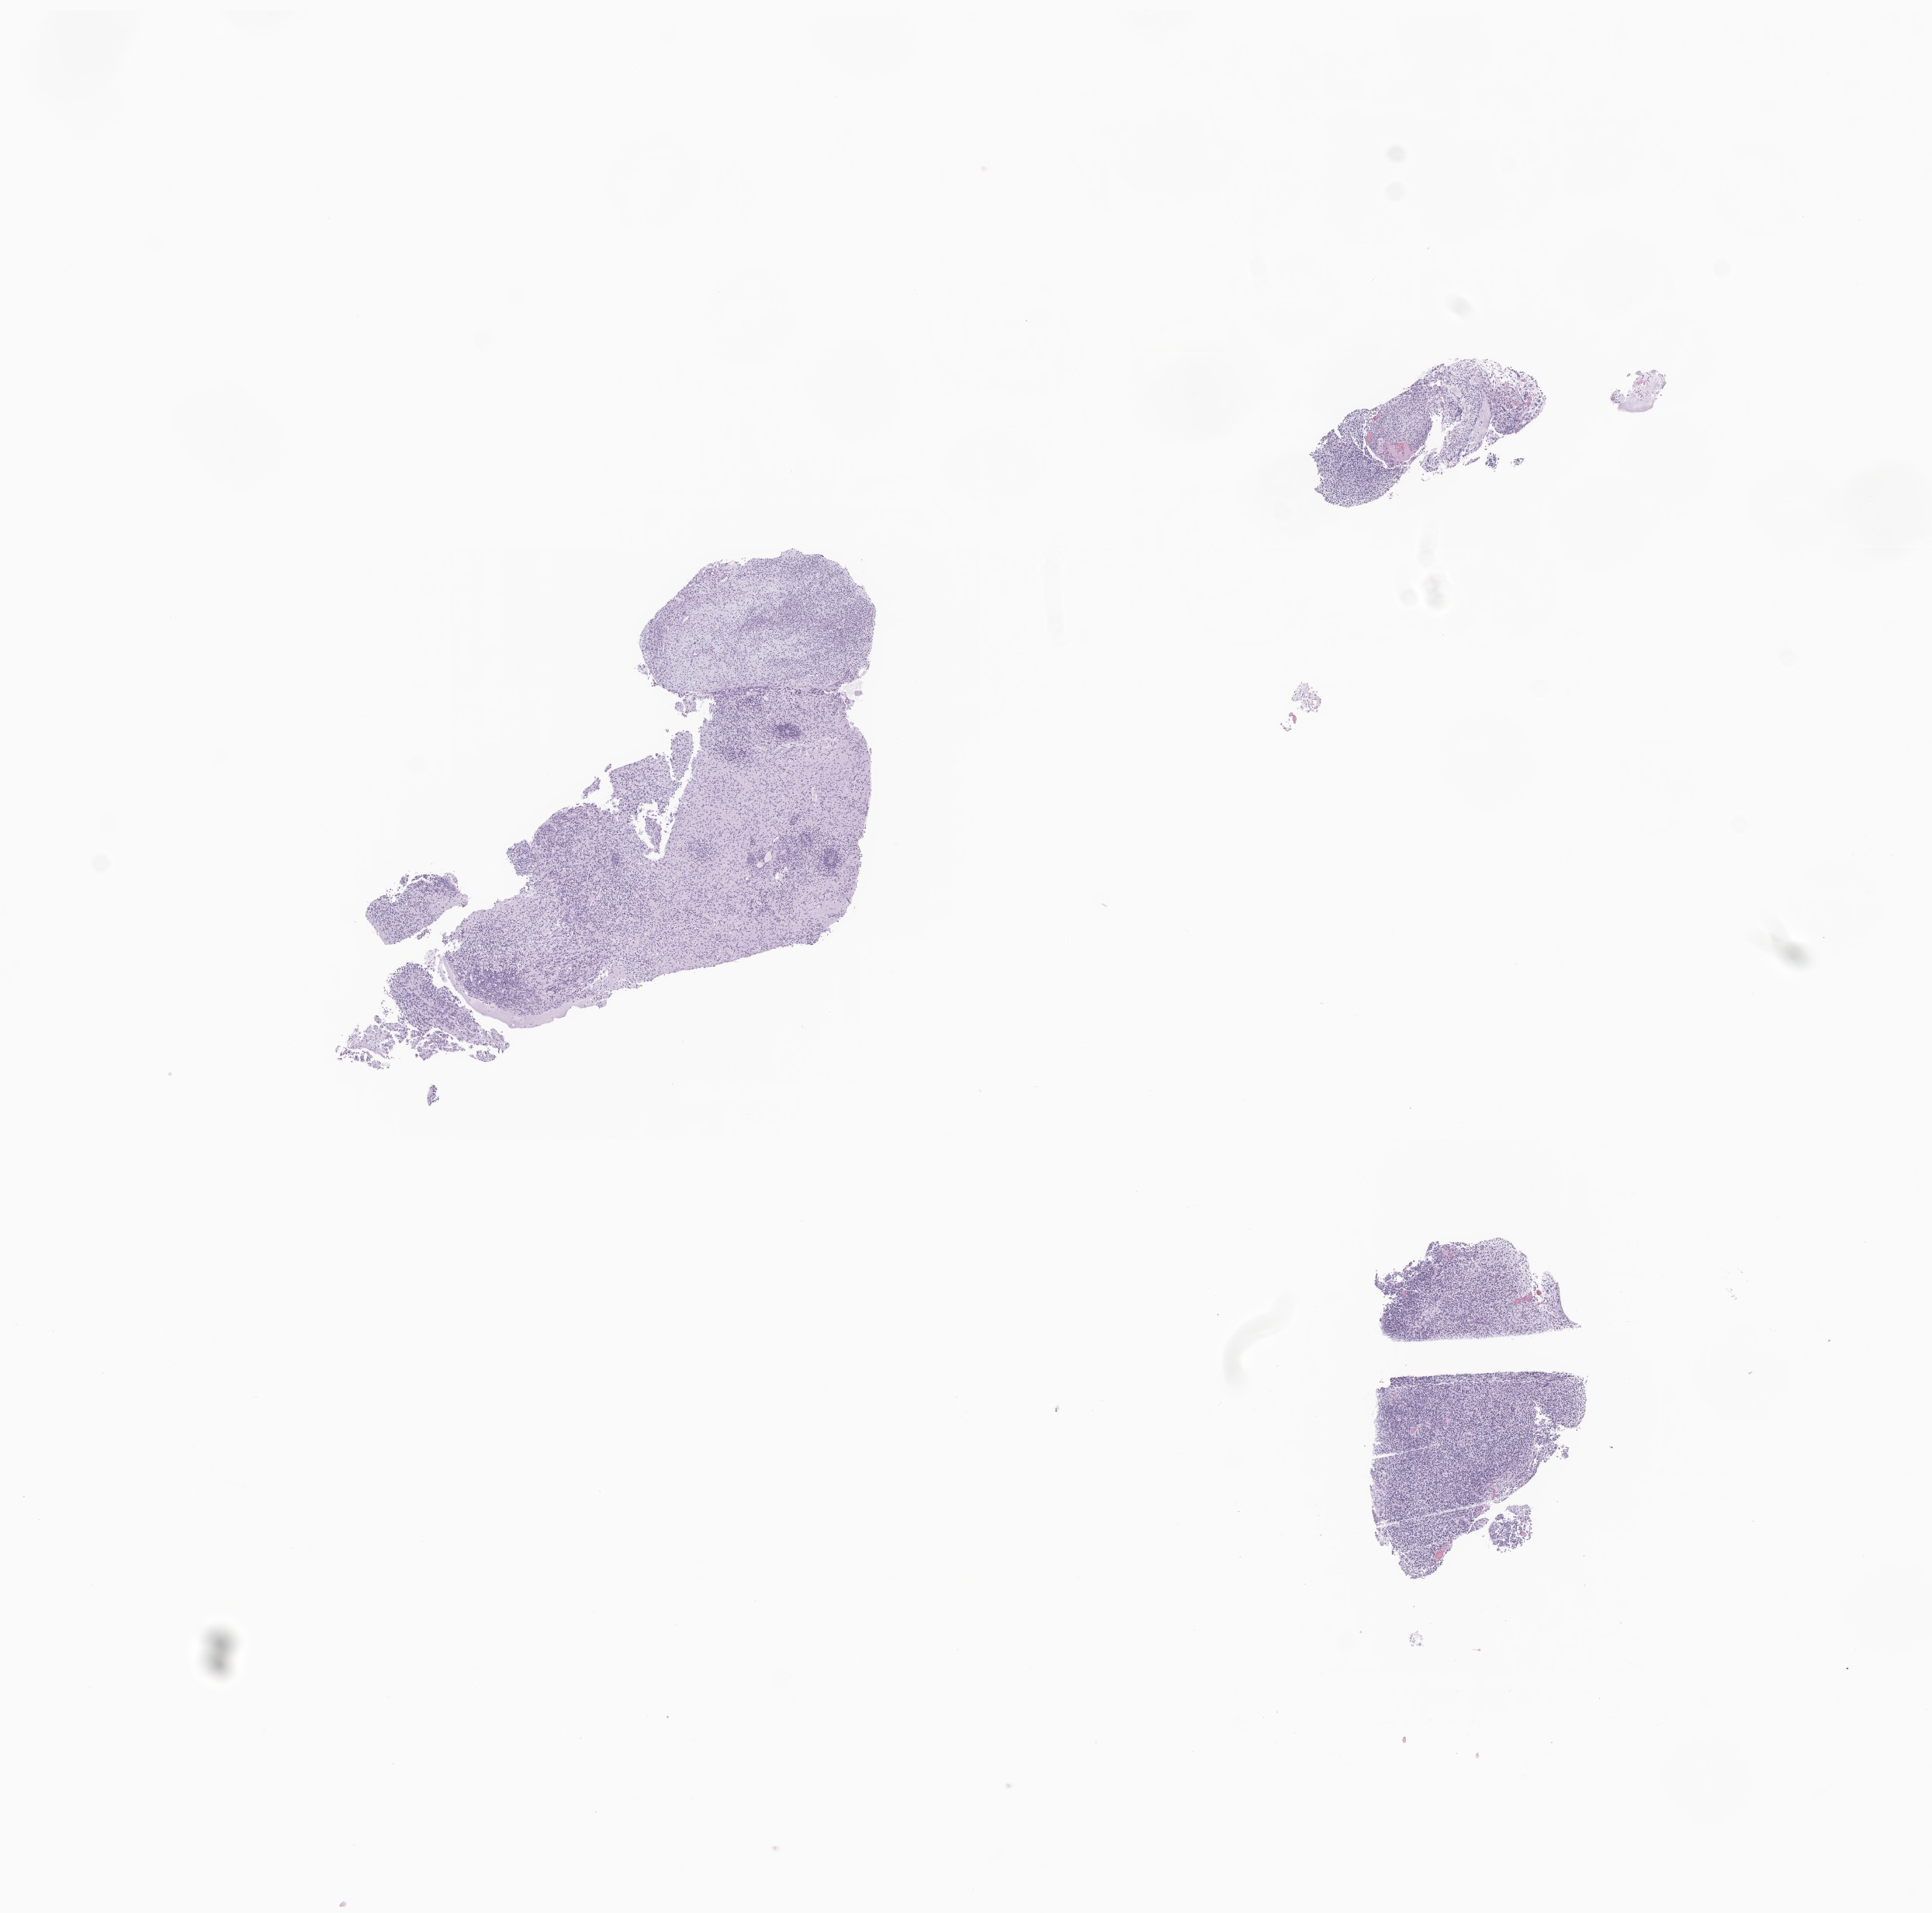
Digitized hematoxylin and eosin (H&E)-stained section of tumor tissue from the brain, whole scanned area (about 10.5 x 10.4 mm) shown as a low-resolution overview; formalin-fixed paraffin-embedded section. Male patient, age 27 days.
Recorded diagnosis: Neoplasm, uncertain whether benign or malignant.